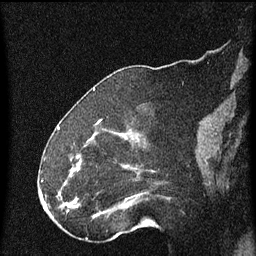
Breast MRI (dynamic contrast-enhanced), one sagittal slice; dynamic contrast-enhanced series, image 2 of 4 at this slice position (ordered by acquisition); 1.5 T; TE 4.2 ms, TR 8 ms; 2 mm slice thickness; 256 × 256 image matrix. Female patient, age 52 years.
Structures marked on this image (semi-automatic segmentation, software-assisted and operator-edited):
- analysis volume of interest (the breast-tissue region the enhancement analysis was run in; not a lesion): bounding box [x1, y1, x2, y2] px = [73, 154, 168, 219]
- tumour enhancement mask (voxels above the 70 % enhancement threshold inside the analysis volume of interest): [73, 170, 100, 215]